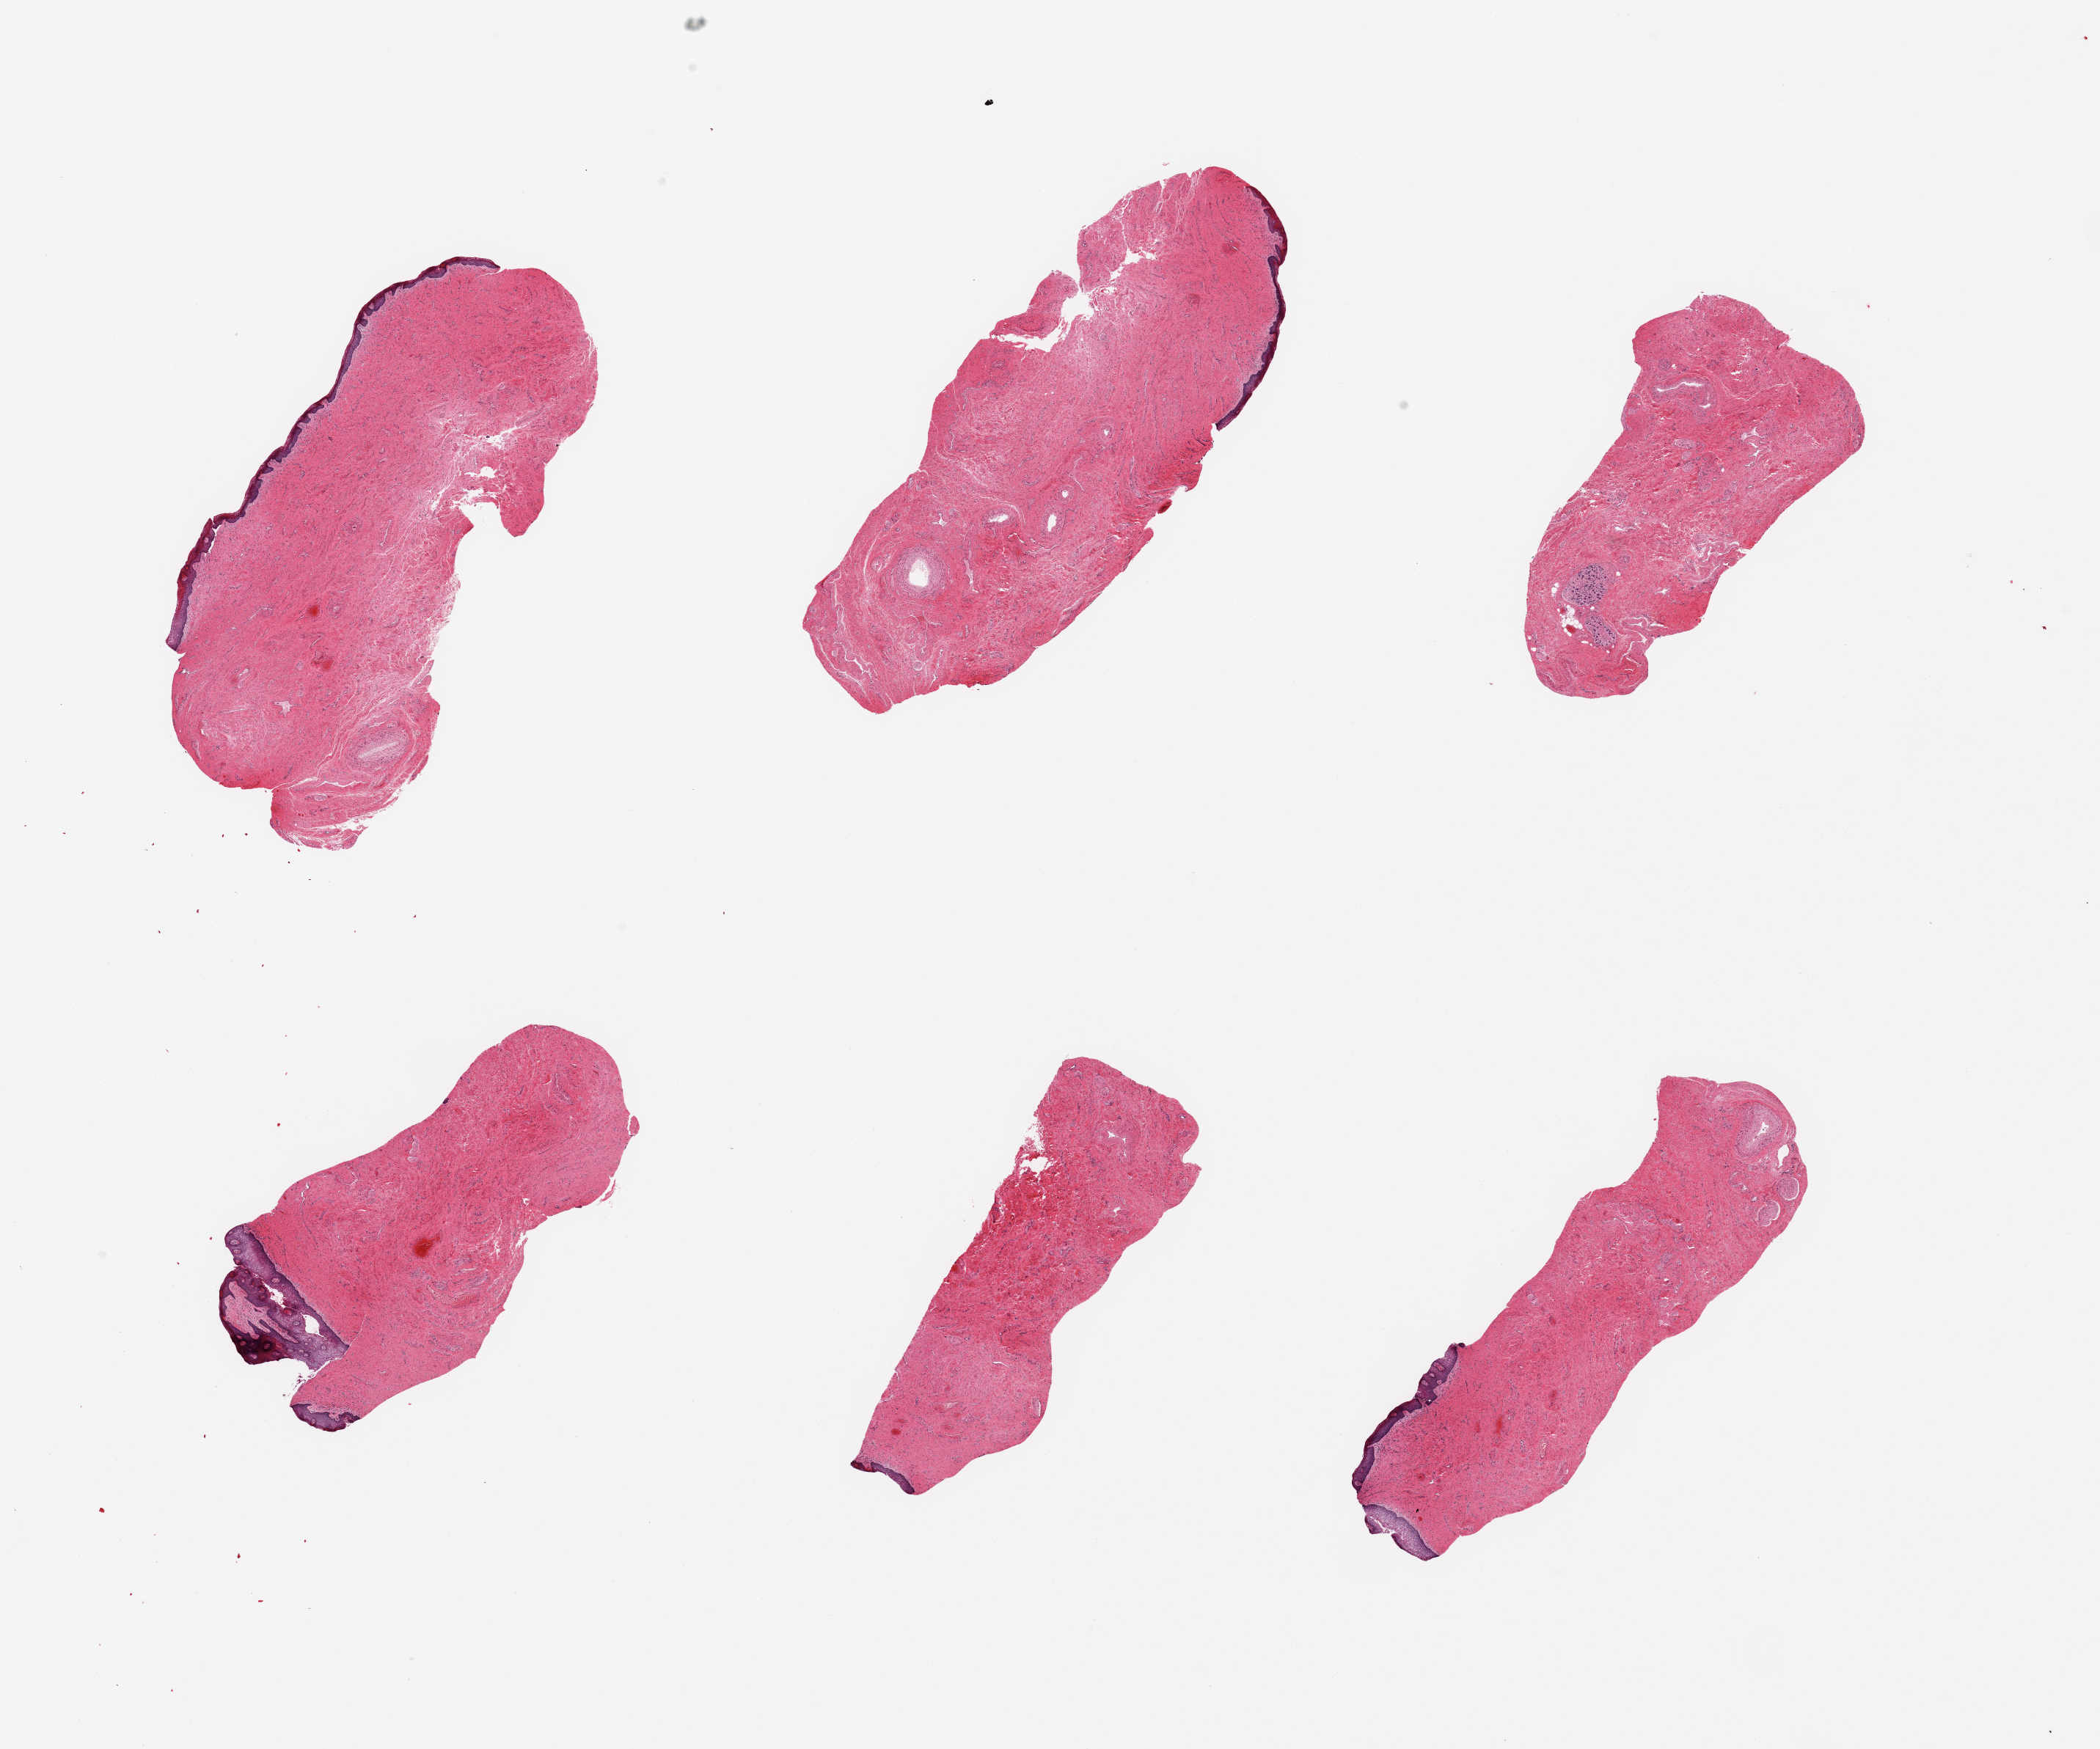
Hematoxylin and eosin (H&E) whole-slide image — a low-resolution overview of the entire scanned area, about 22.6 x 18.9 mm (from a 20x scan), PAXgene-fixed, paraffin-embedded tissue, target tissue: vagina, donor tissue sample. Donor sex: female.
- reviewer comment on this tissue sample: 6 pieces